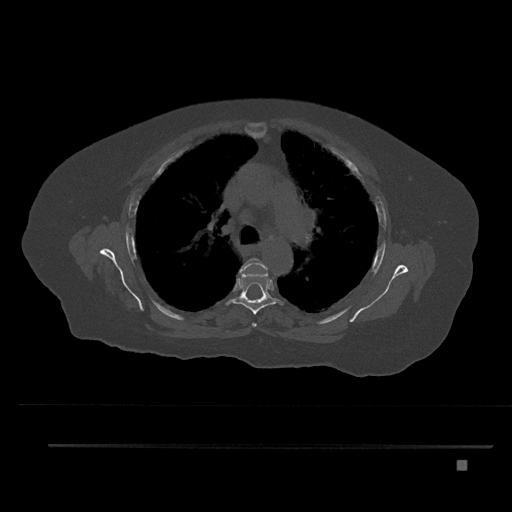
CT including the spine, one axial slice; position 572 of 797 along the scan axis; reconstruction kernel Br40s/3; 120 kVp; bone window (W 1800 / L 400 HU); 0.5 mm slice thickness; 512 × 512 image matrix, field of view 437 × 437 mm. Patient: female, 76 years. From the clinical record (not read from this slice): primary cancer: lung; vertebrae with lytic lesions (as recorded): T11, L3.
Structures marked on this image (semi-automatically segmented with operator editing):
- T4 vertebra: bounding box [x1, y1, x2, y2] px = [240, 258, 268, 327]
- T5 vertebra: [226, 273, 284, 314]